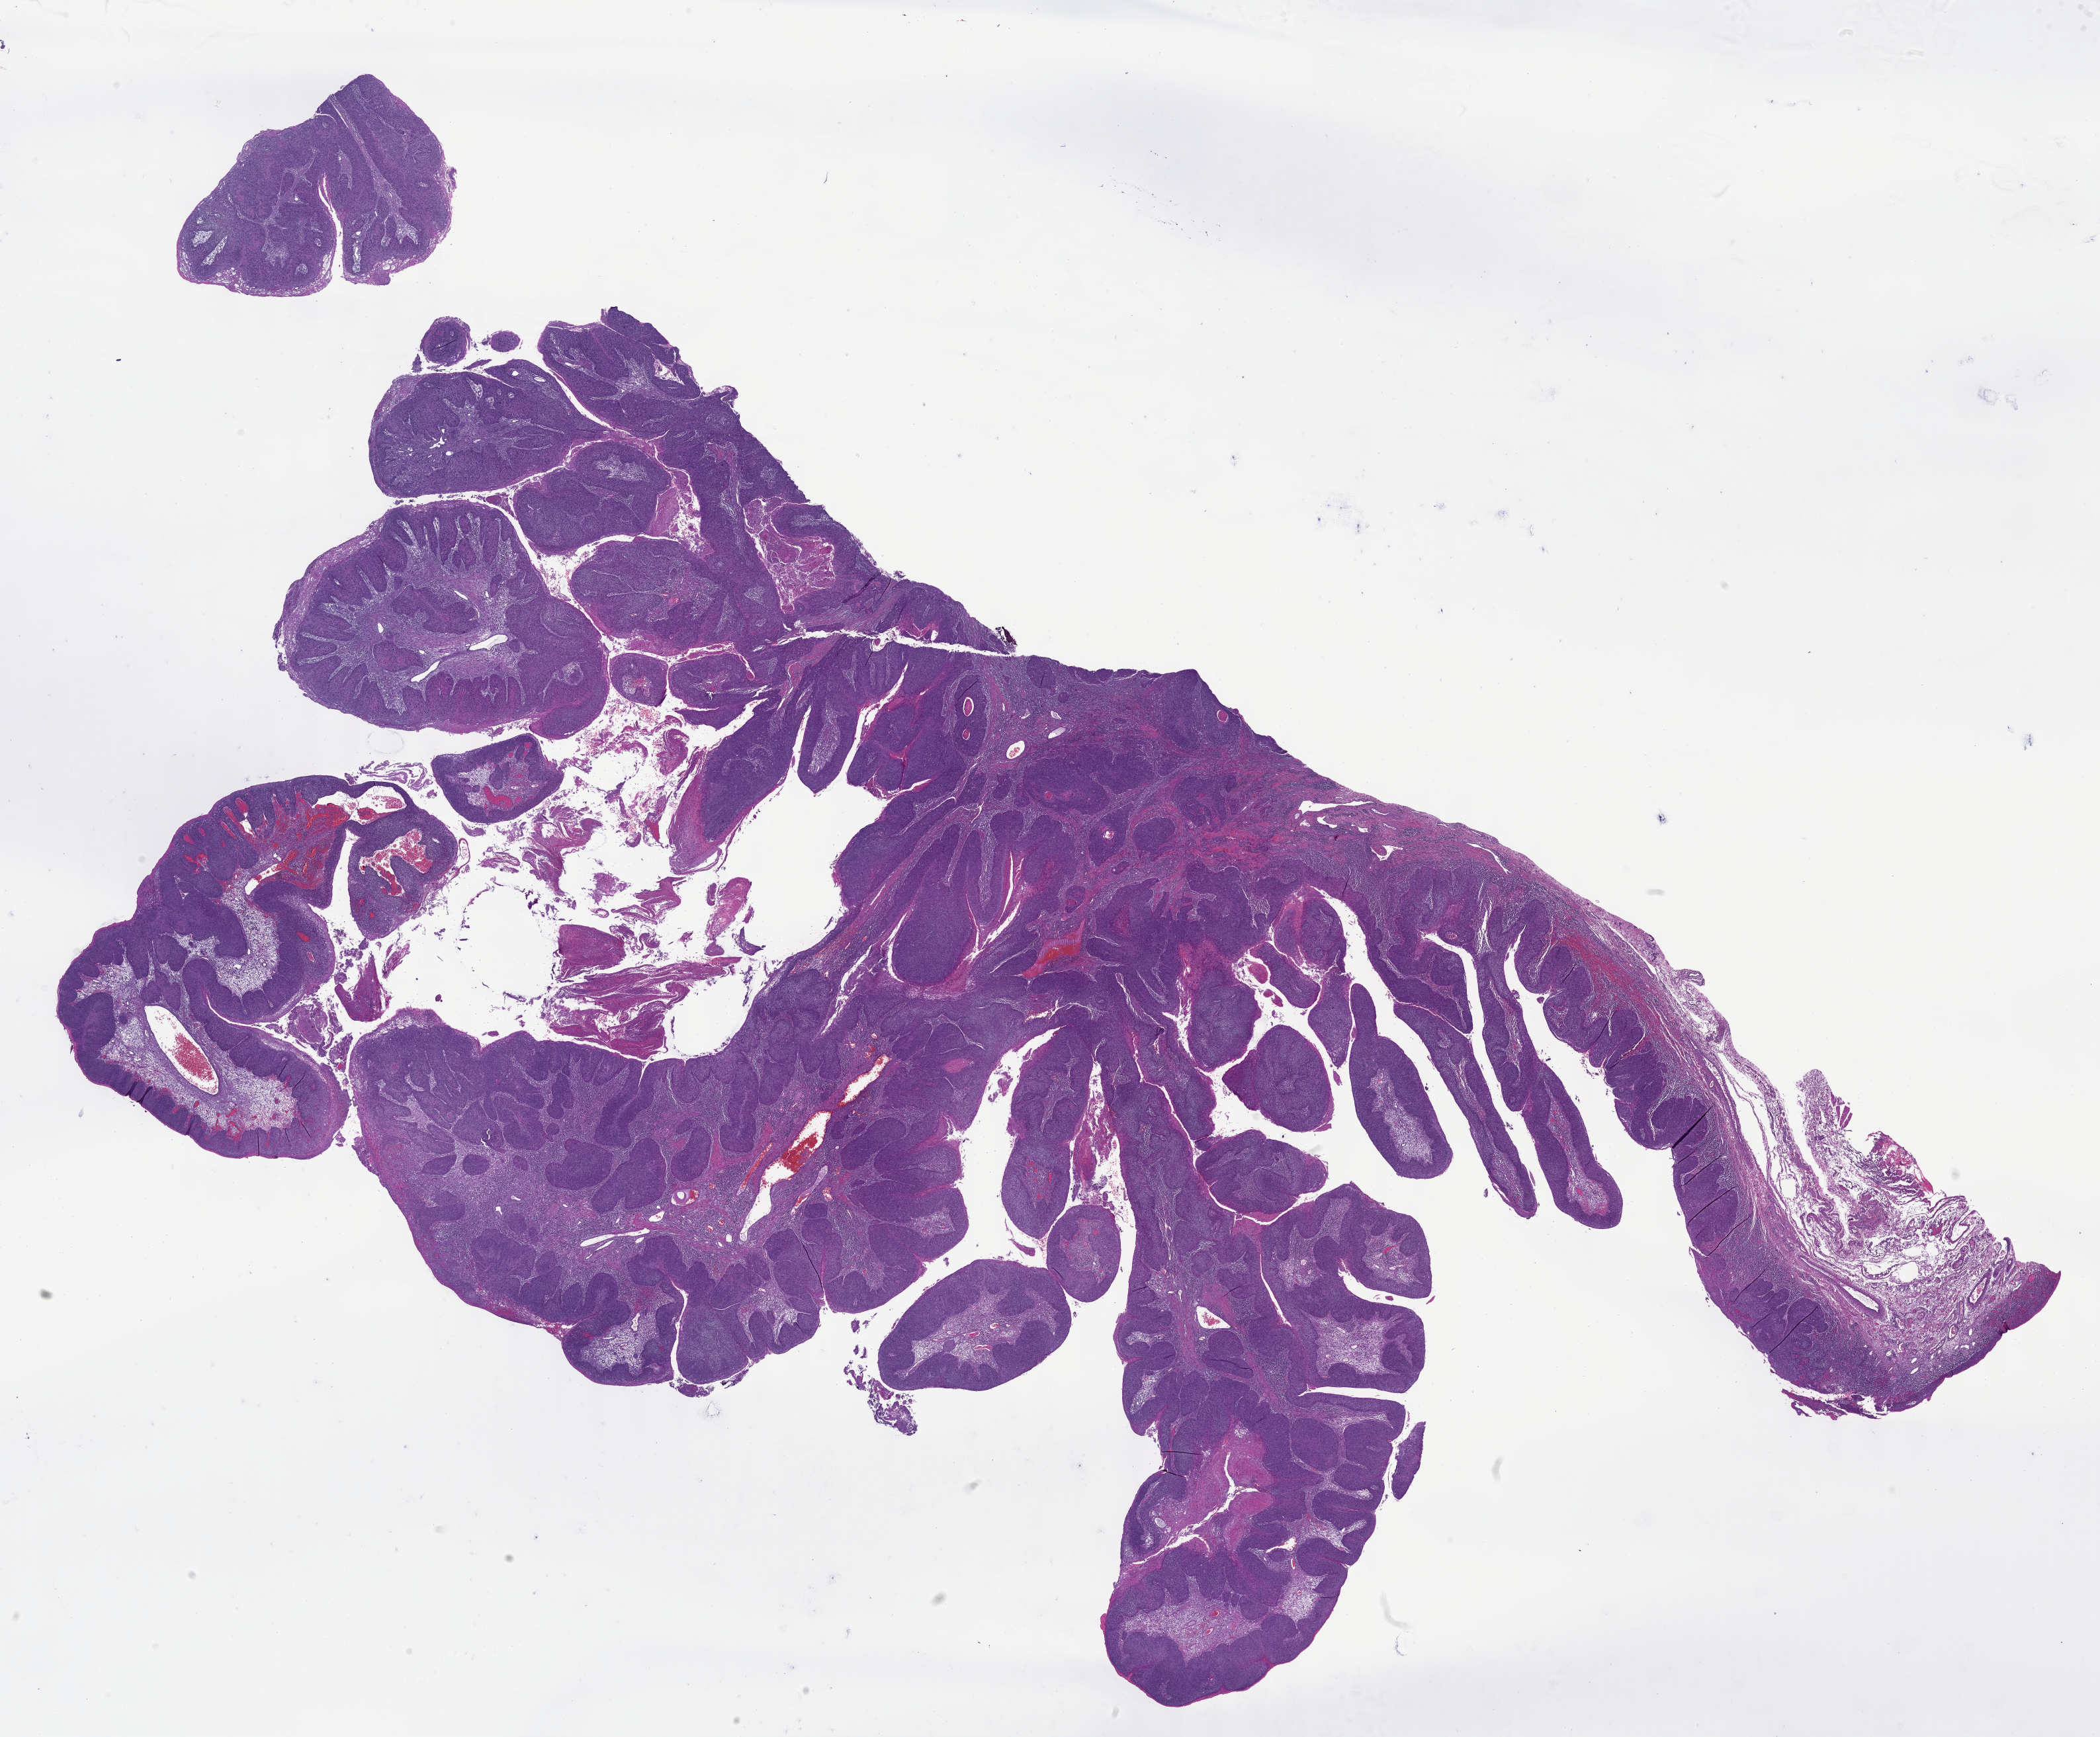
Digitized H&E-stained tissue section (whole slide), shown as a low-resolution overview of the whole scanned area (about 25.7 x 21.2 mm, acquisition: 40x scan). Formalin-fixed paraffin-embedded (FFPE) diagnostic section. Primary tumour sample from the head and neck. Female patient; age at initial diagnosis 76 years. Histologic grade: G3 (poorly differentiated).
AJCC pathologic stage: IVA (7th edition). Histologic diagnosis: Squamous cell carcinoma, NOS.